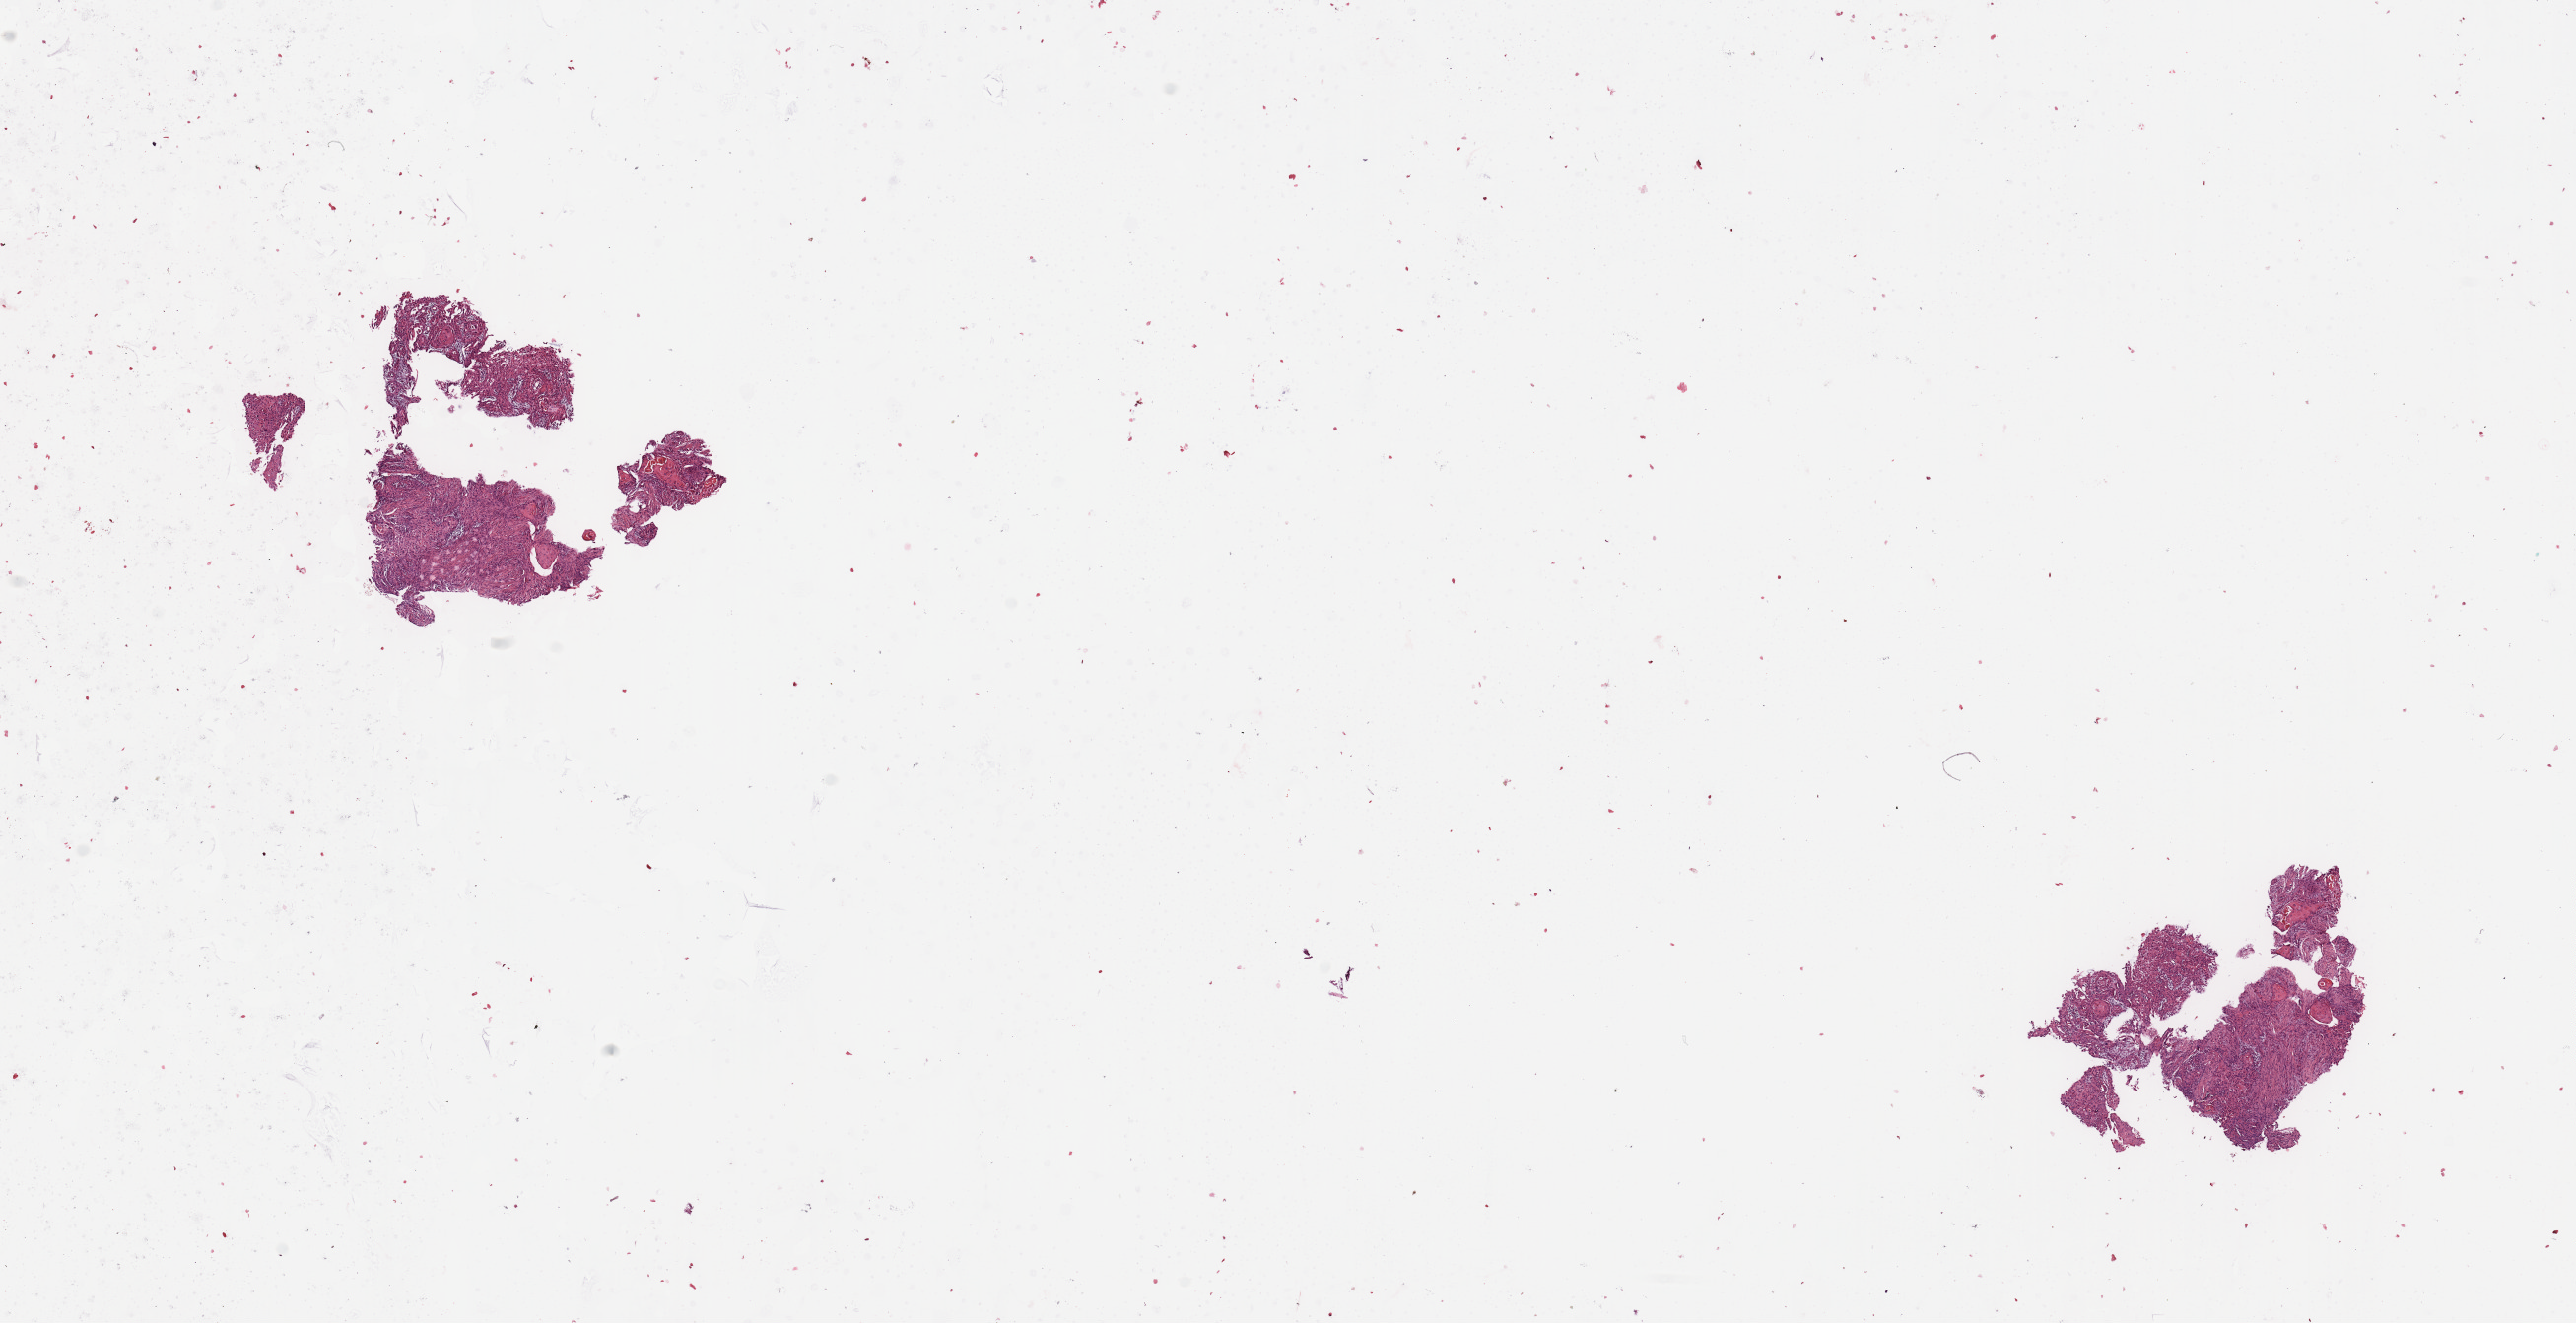
H&E whole-slide image, shown as a low-resolution overview of the whole scanned area (about 20.7 x 10.6 mm, slide scanned at 20x). Tumour tissue sample, sampled site: larynx. Patient: male, age 72 years. Histologic grade: G2 (moderately differentiated). Composition of this section per pathologist review: tumour nuclei 80%, necrosis 2%.
Histologic diagnosis: Squamous cell carcinoma, NOS (larynx, NOS). AJCC pathologic stage: IVA.